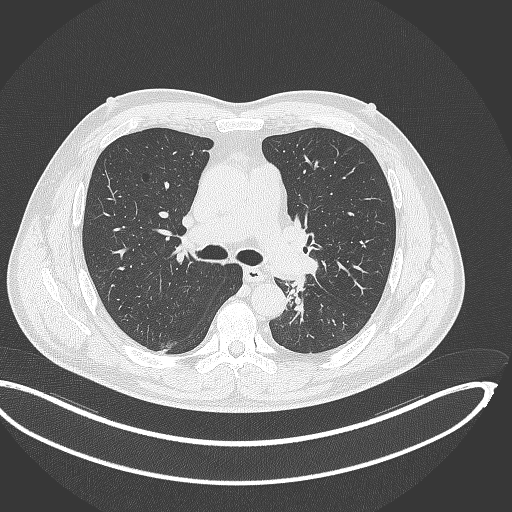
Chest CT, one axial slice. Slice 221 of 362 in the series (ordered by position). Reconstruction kernel B70f. 120 kVp. Lung window (W 1500 / L -600 HU). 512 × 512 image matrix, field of view 442 × 442 mm. Patient: male, 50 years. Case-level facts recorded for this patient, not image findings: clinical TNM (as recorded): T2a N3 M0.
Annotated regions visible in this slice (bounding box drawn by a radiologist):
- lung tumour (recorded histology: squamous cell carcinoma): bounding box [x1, y1, x2, y2] px = [284, 275, 309, 324]